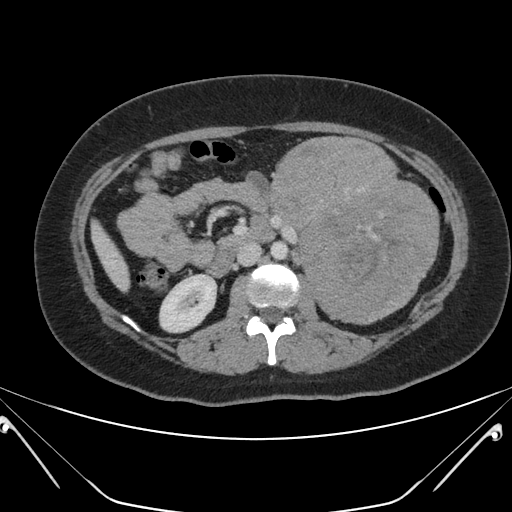
Contrast-enhanced abdominal CT, one axial slice; slice 106 of 168 in the series (ordered by position); 120 kVp; intravenous contrast given; soft-tissue window (W 400 / L 40 HU); 3 mm slice thickness; 512 × 512 image matrix, field of view 394 × 394 mm. Female patient, age 26 years. From the clinical record (not read from this slice): diagnosis: adrenocortical carcinoma; tumour side: left adrenal; tumour size at pathology: 28 cm; Ki-67 index: 20 %; stage (as recorded): 2.
Outlined on this slice (semi-automatic segmentation, software-assisted and operator-edited):
- mass: box from (x=271, y=136) to (x=439, y=324) px